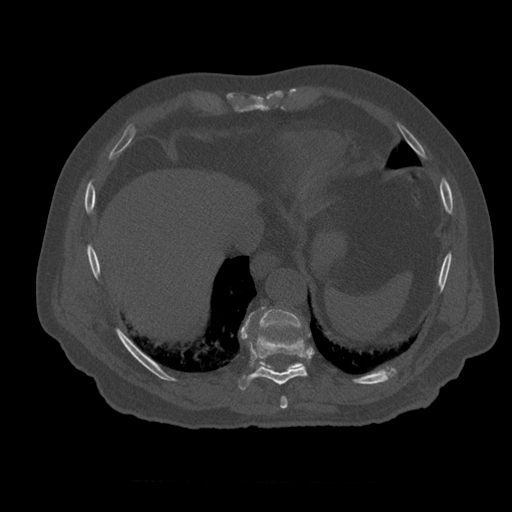
CT including the spine, one axial slice. Position 317 of 399 along the scan axis. Reconstruction kernel STANDARD. 120 kVp. Bone window (W 1800 / L 400 HU). 512 × 512 image matrix, field of view 407 × 407 mm. Patient age 73 years. From the clinical record (not read from this slice): primary cancer: prostate.
Structures marked on this image (semi-automatic segmentation, software-assisted and operator-edited):
- T10 vertebra: bounding box (x1, y1, x2, y2) in pixels: (259, 307, 303, 369)
- T8 vertebra: (281, 396, 288, 409)
- T9 vertebra: (239, 313, 311, 391)